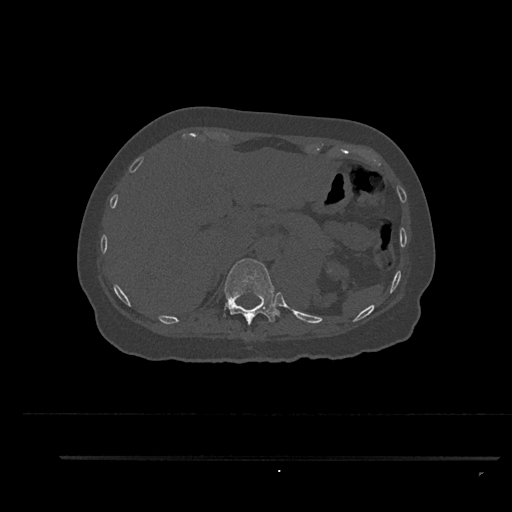
CT including the spine, one axial slice; slice 316 of 797 in the series (ordered by position); bone window (W 1800 / L 400 HU); 512 × 512 image matrix. Patient: female, 44 years. From the clinical record (not read from this slice): primary cancer: renal; vertebrae with lytic lesions (as recorded): L1.
Structures marked on this image (semi-automatic segmentation, software-assisted and operator-edited):
- T11 vertebra: bounding box <224,259,280,326> (left, top, right, bottom; pixels)